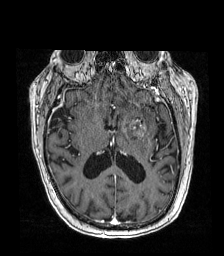
Brain MRI from a brain-tumour surgery series, one axial slice; position 84 of 192 along the scan axis; T1-weighted post-contrast; 1 mm slice thickness; 224 × 256 image matrix. From the clinical record (not read from this slice): histopathology: Metastatic carcinoma from lung primary; tumour location: Left Frontal Caudate.
Structures marked on this image (manually delineated by an expert):
- tumour: box from (x=117, y=115) to (x=148, y=139) px